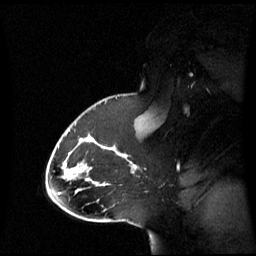
Breast MRI (dynamic contrast-enhanced), one sagittal slice; dynamic contrast-enhanced series, image 2 of 3 at this slice position (ordered by acquisition); 1.5 T; TE 4.2 ms, TR 8.4 ms; 256 × 256 image matrix, field of view 270 × 270 mm. Female patient, age 43 years. Case-level facts recorded for this patient, not image findings: setting: breast cancer imaged before/during neoadjuvant chemotherapy; receptor status: triple-negative.
Outlined on this slice (semi-automatically segmented with operator editing):
- analysis volume of interest (the breast-tissue region the enhancement analysis was run in; not a lesion): bounding box (x1, y1, x2, y2) in pixels: (65, 118, 143, 197)
- tumour enhancement mask (voxels above the 70 % enhancement threshold inside the analysis volume of interest): (115, 147, 136, 168)